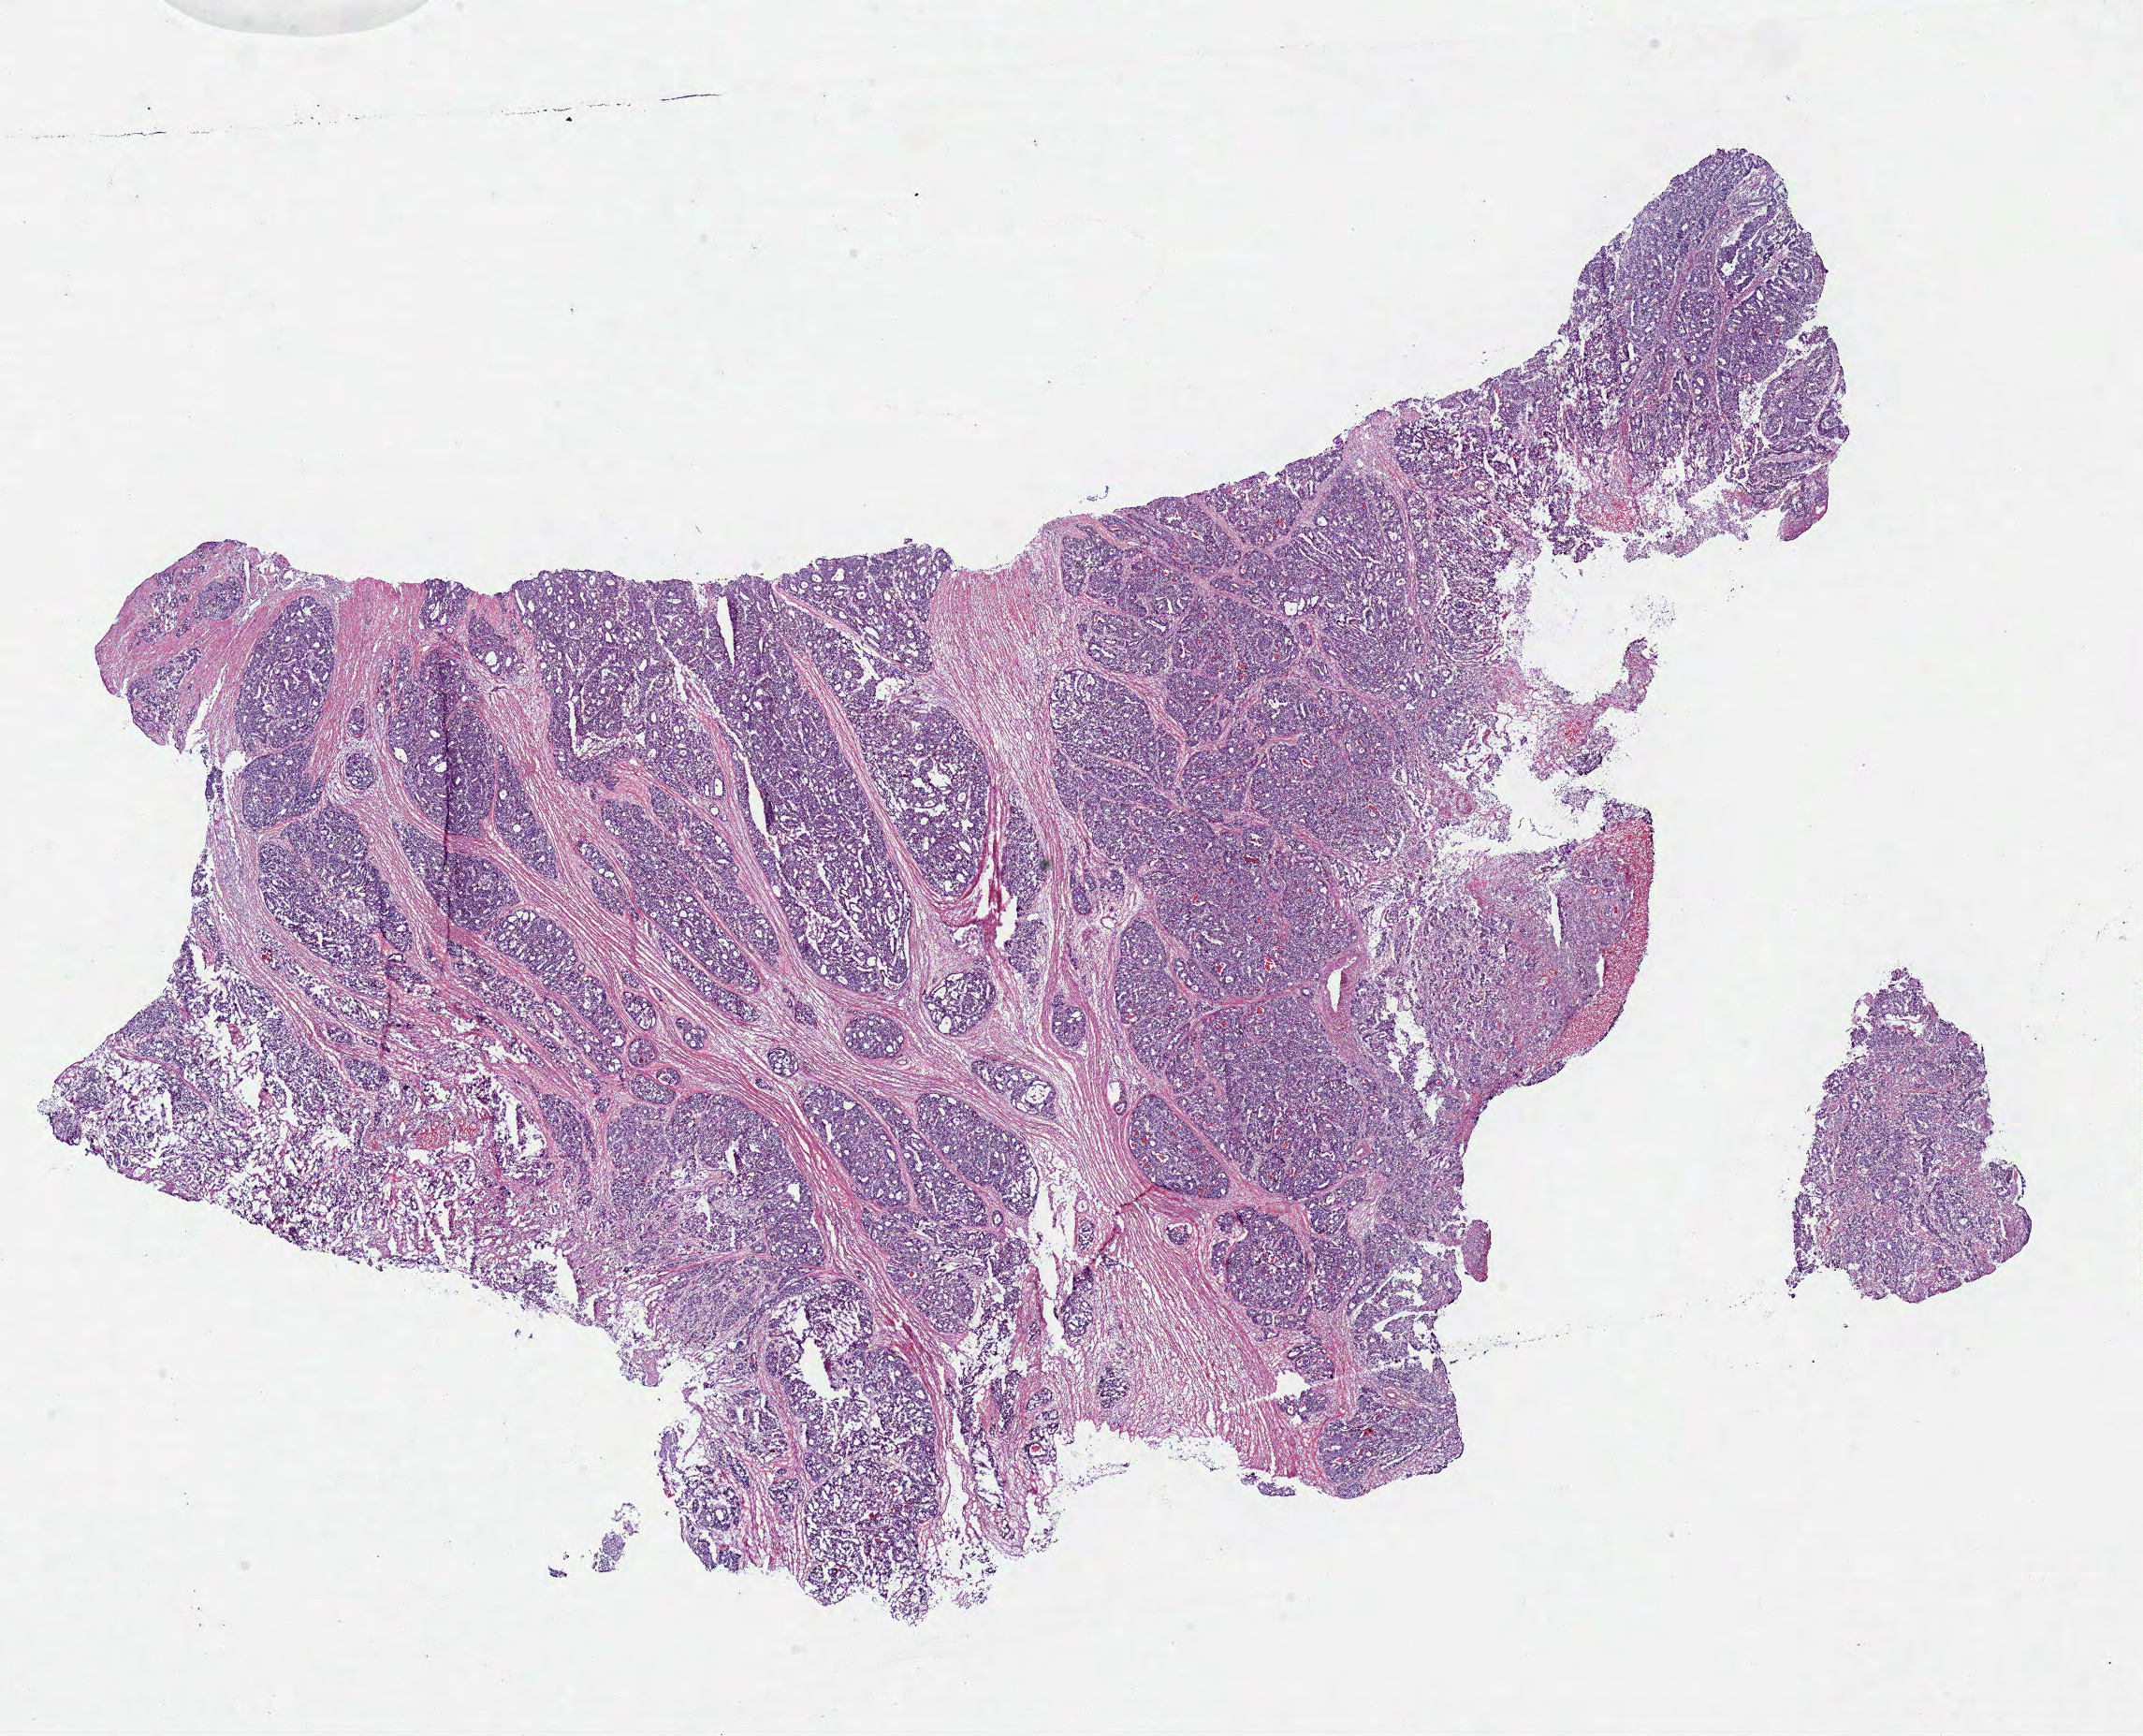
Whole-slide histology image, Hematoxylin and eosin (H&E) stained, shown as a low-resolution overview of the whole scanned area (about 18.0 x 14.6 mm, slide scanned at 40x). Frozen section from the bottom of the tissue portion. Primary tumour sample from the colon. Male patient; age at initial diagnosis 80 years. Slide review estimates, as recorded: tumour cells 99%, tumour nuclei 80%, normal cells 0%, stromal cells 0%, necrosis 1%. Infiltration values recorded for this section: lymphocyte infiltration 5%, monocyte infiltration 0%, neutrophil infiltration 0%.
Diagnosis: Adenocarcinoma, NOS (ascending colon). AJCC pathologic stage: IVA. Lymph nodes positive (case pathology): 1 of 24 examined.